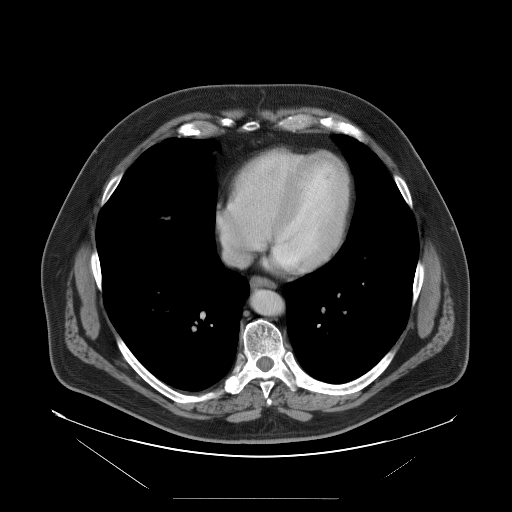
Contrast-enhanced abdominal CT, one axial slice; position 102 of 114 along the scan axis; 120 kVp; intravenous contrast given; soft-tissue window (W 400 / L 40 HU); 5 mm slice thickness; 512 × 512 image matrix. Male patient, age 61 years. Case-level facts recorded for this patient, not image findings: diagnosis: colorectal cancer liver metastases, imaged before liver resection; multiple liver metastases: no; largest metastasis: 6.5 cm; disease in both lobes: yes.
Outlined on this slice (manually delineated by an expert):
- hepatic veins: bounding box [x1, y1, x2, y2] px = [218, 214, 268, 265]